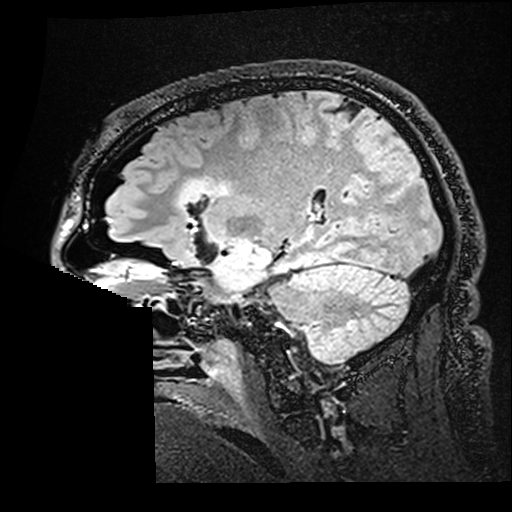
Brain MRI from a brain-tumour surgery series, one sagittal slice; T2 FLAIR; 1 mm slice thickness; 512 × 512 image matrix. From the clinical record (not read from this slice): histopathology: Astrocytoma; WHO grade: 2; IDH mutation: yes.
Outlined on this slice (manually delineated by an expert):
- residual tumour: bounding box (x1, y1, x2, y2) in pixels: (178, 179, 232, 208)